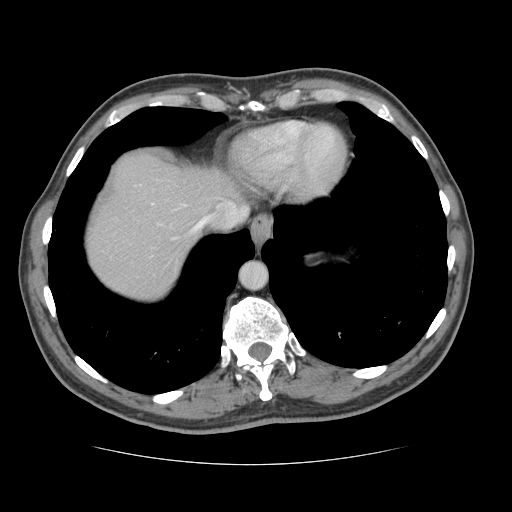
Contrast-enhanced abdominal CT, one axial slice; slice 115 of 134 in the series (ordered by position); intravenous contrast given; soft-tissue window (W 400 / L 40 HU); 2.5 mm slice thickness; 512 × 512 image matrix, field of view 377 × 377 mm. Male patient, age 68 years. Case-level facts recorded for this patient, not image findings: diagnosis: colorectal cancer liver metastases, imaged before liver resection; multiple liver metastases: yes; largest metastasis: 2.2 cm; disease in both lobes: no.
Outlined on this slice (manually delineated by an expert):
- hepatic veins: bounding box (x1, y1, x2, y2) in pixels: (152, 202, 247, 231)
- liver: (86, 154, 239, 300)
- planned liver remnant (the part of the liver to remain after resection): (86, 155, 239, 297)